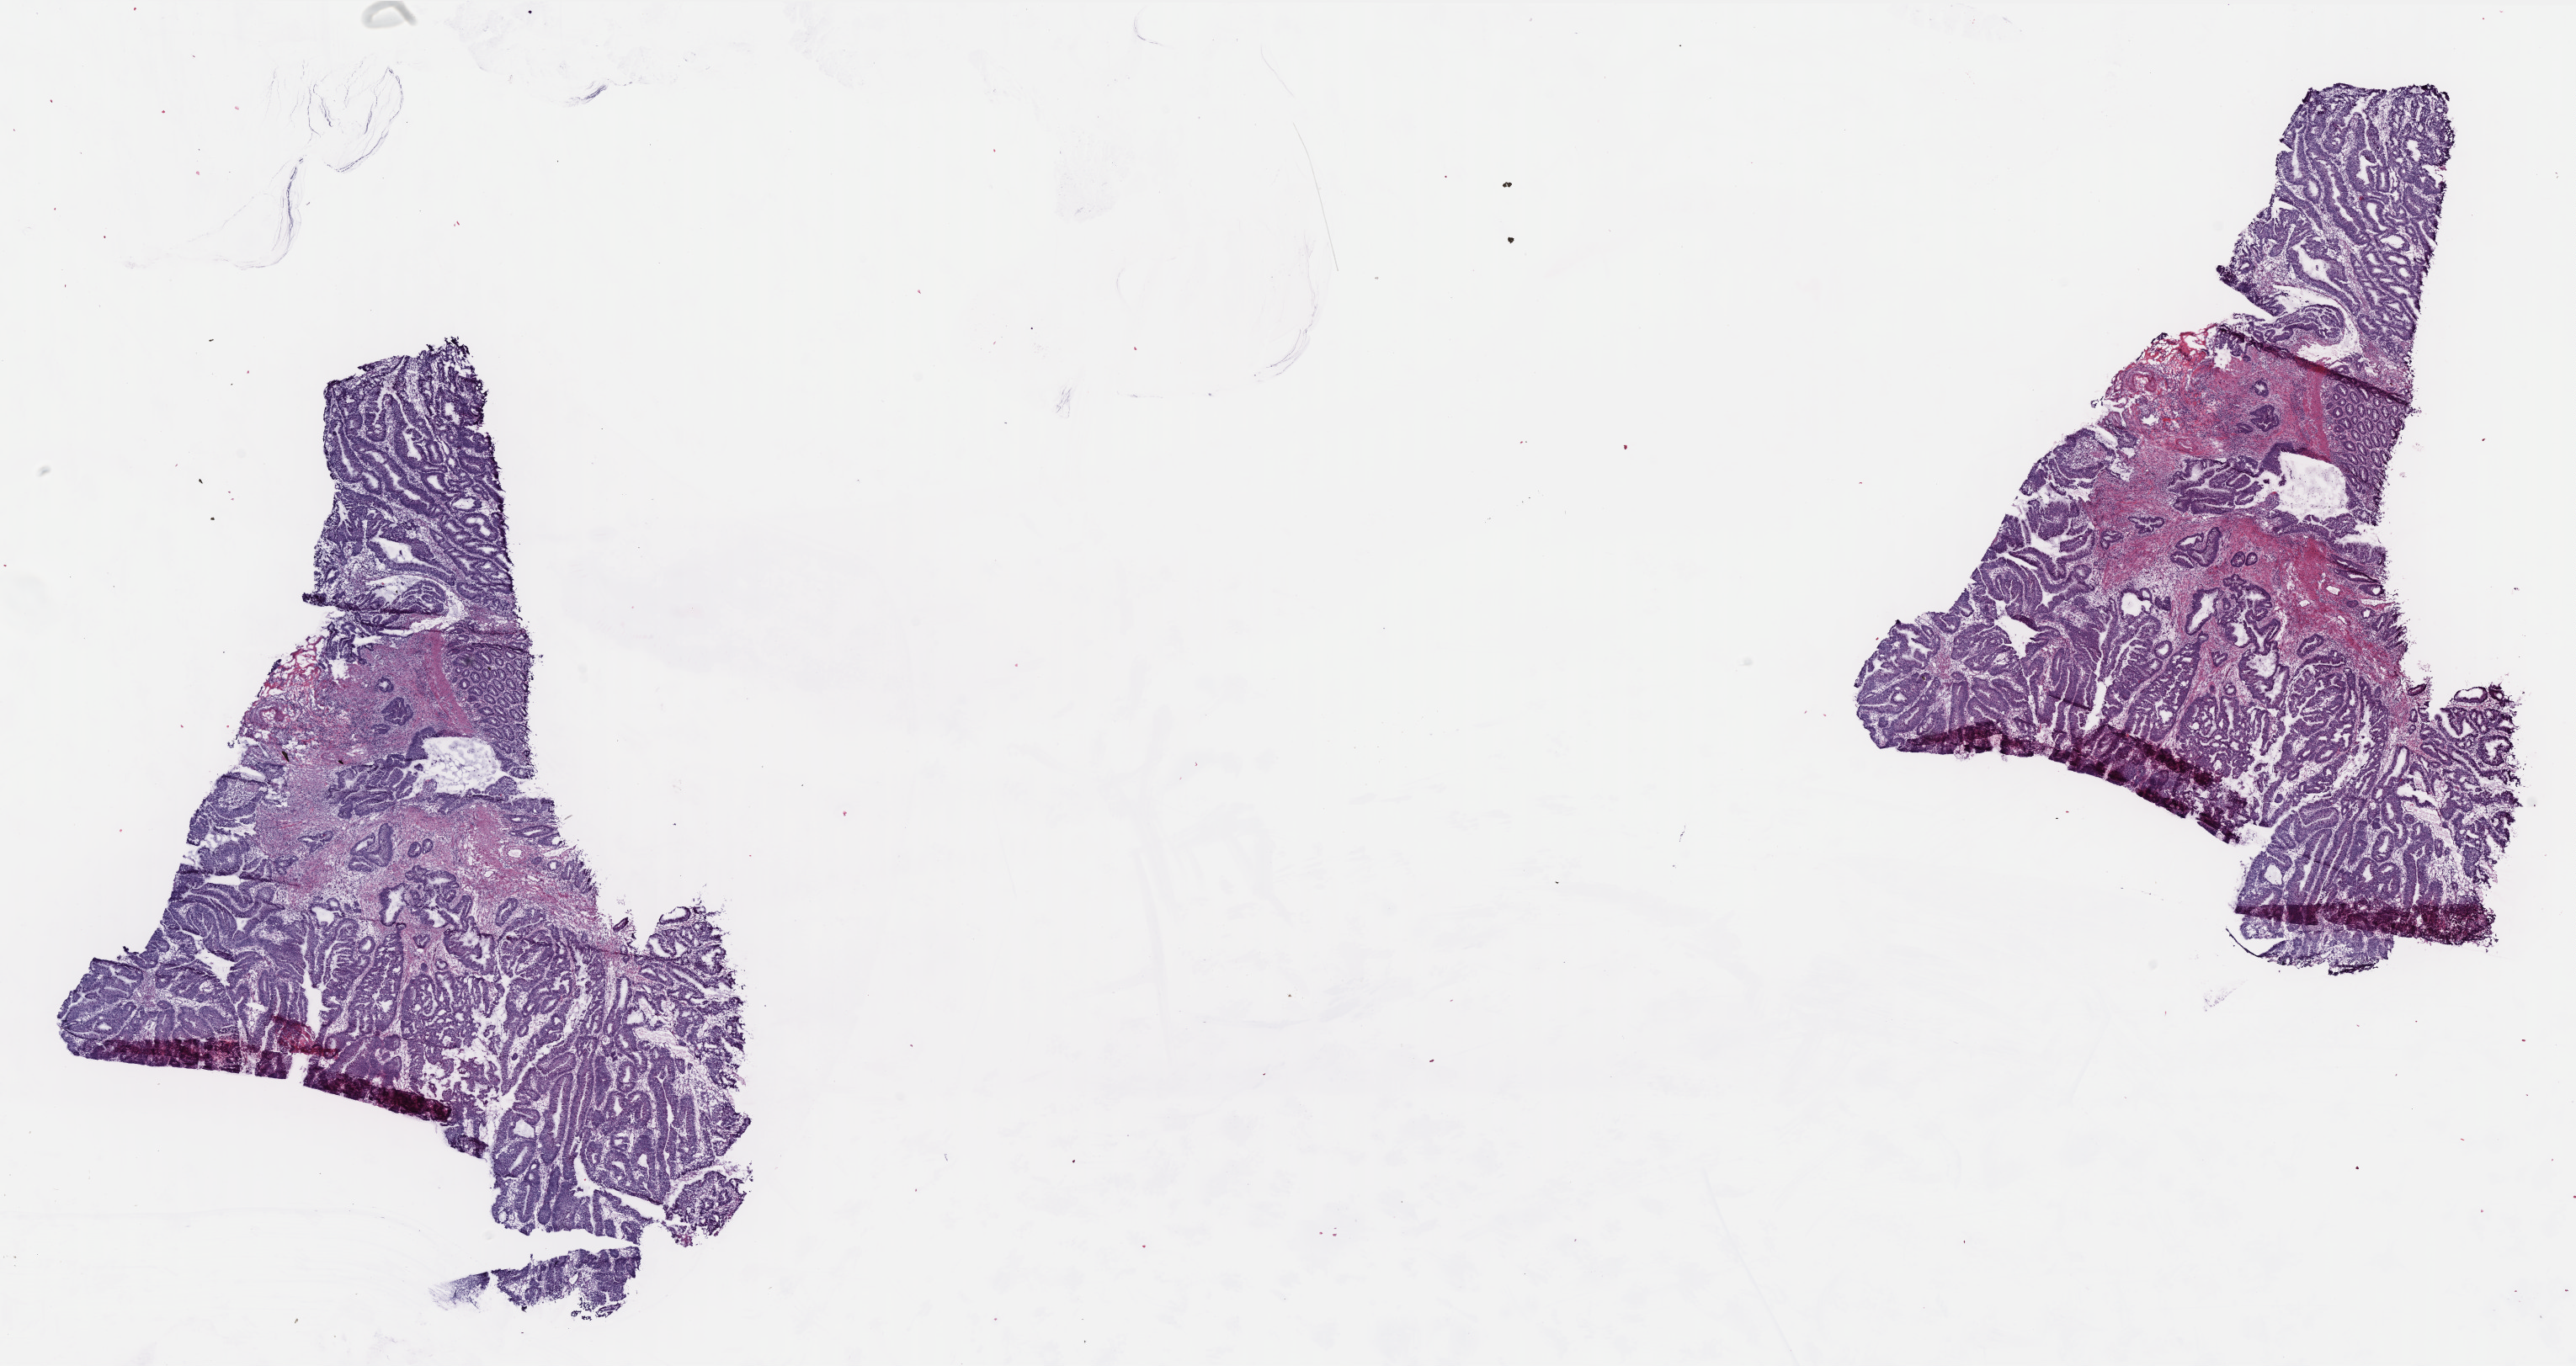
Digitized H&E-stained tissue section (whole slide), shown as a low-resolution overview of the whole scanned area (about 24.5 x 13.0 mm, slide scanned at 40x). Frozen section from the bottom of the tissue portion. Primary tumour sample from the rectum. Patient: female, age at initial diagnosis 50 years. Composition of this section per pathologist review: tumour cells 70%, tumour nuclei 80%, normal cells 5%, stromal cells 24%, necrosis 1%. Infiltration values recorded for this section: lymphocyte infiltration 2%, monocyte infiltration 2%, neutrophil infiltration 0%.
- AJCC pathologic stage: I (6th edition)
- lymph nodes positive (case pathology): 0 of 28 examined
- diagnosis: Mucinous adenocarcinoma